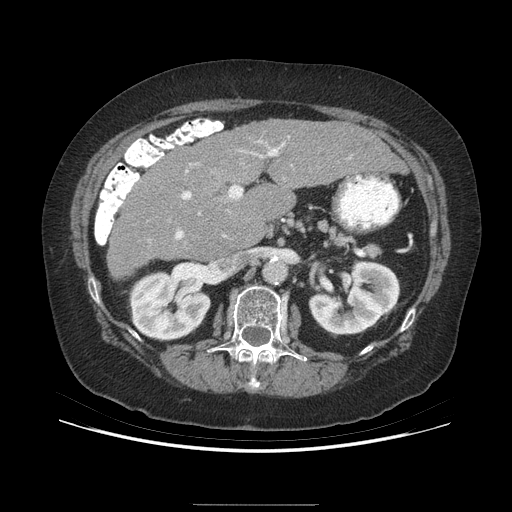
Contrast-enhanced abdominal CT (liver protocol), one axial slice; position 148 of 192 along the scan axis; soft-tissue window (W 400 / L 40 HU); 512 × 512 image matrix. Case-level facts recorded for this patient, not image findings: diagnosis: hepatocellular carcinoma (patient treated with transarterial chemoembolisation; whether this scan precedes or follows treatment is not stated here); TNM stage (as recorded): Stage-I; Child-Pugh class: A; tumour size: 3.2 cm.
Outlined on this slice (semi-automatically segmented with operator editing):
- liver parenchyma outside the tumour (the mass and vessels are separate outlines, so this box may not span the whole liver): bounding box [x1, y1, x2, y2] px = [108, 118, 404, 276]
- liver vessels: [175, 141, 284, 240]